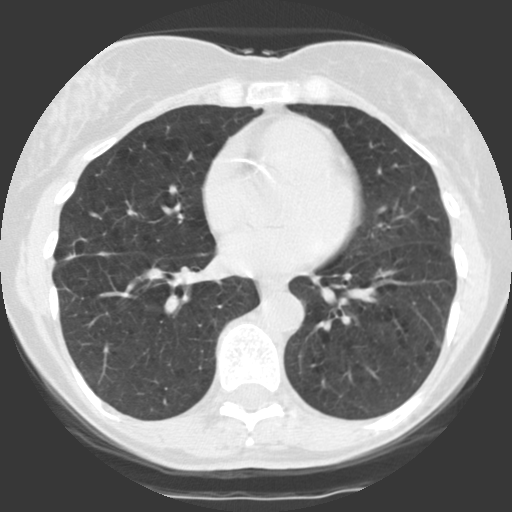
Low-dose screening chest CT, one axial slice; slice 54 of 123 in the series (ordered by position); 140 kVp; lung window (W 1500 / L -600 HU); 512 × 512 image matrix.
Annotated regions visible in this slice (expert manual segmentation):
- lesion 1 (tumor, middle lobe of right lung): bounding box (x1, y1, x2, y2) in pixels: (65, 253, 77, 260)